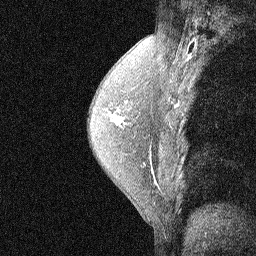
Breast MRI (dynamic contrast-enhanced), one sagittal slice; dynamic contrast-enhanced study with each time point stored as its own series, time point 2 of 3 at this slice position (early post-contrast, ordered by acquisition time); 1.5 T; TE 4.5 ms, TR 11 ms; 2.07 mm slice thickness; 256 × 256 image matrix. Patient: female, 54 years. From the clinical record (not read from this slice): setting: breast cancer imaged before/during neoadjuvant chemotherapy; receptor status: HR-positive, HER2-negative.
Outlined on this slice (semi-automatic segmentation, software-assisted and operator-edited):
- analysis volume of interest (the breast-tissue region the enhancement analysis was run in; not a lesion): bounding box [x1, y1, x2, y2] px = [92, 89, 149, 186]
- tumour enhancement mask (voxels above the 90 % enhancement threshold inside the analysis volume of interest): [112, 114, 123, 123]